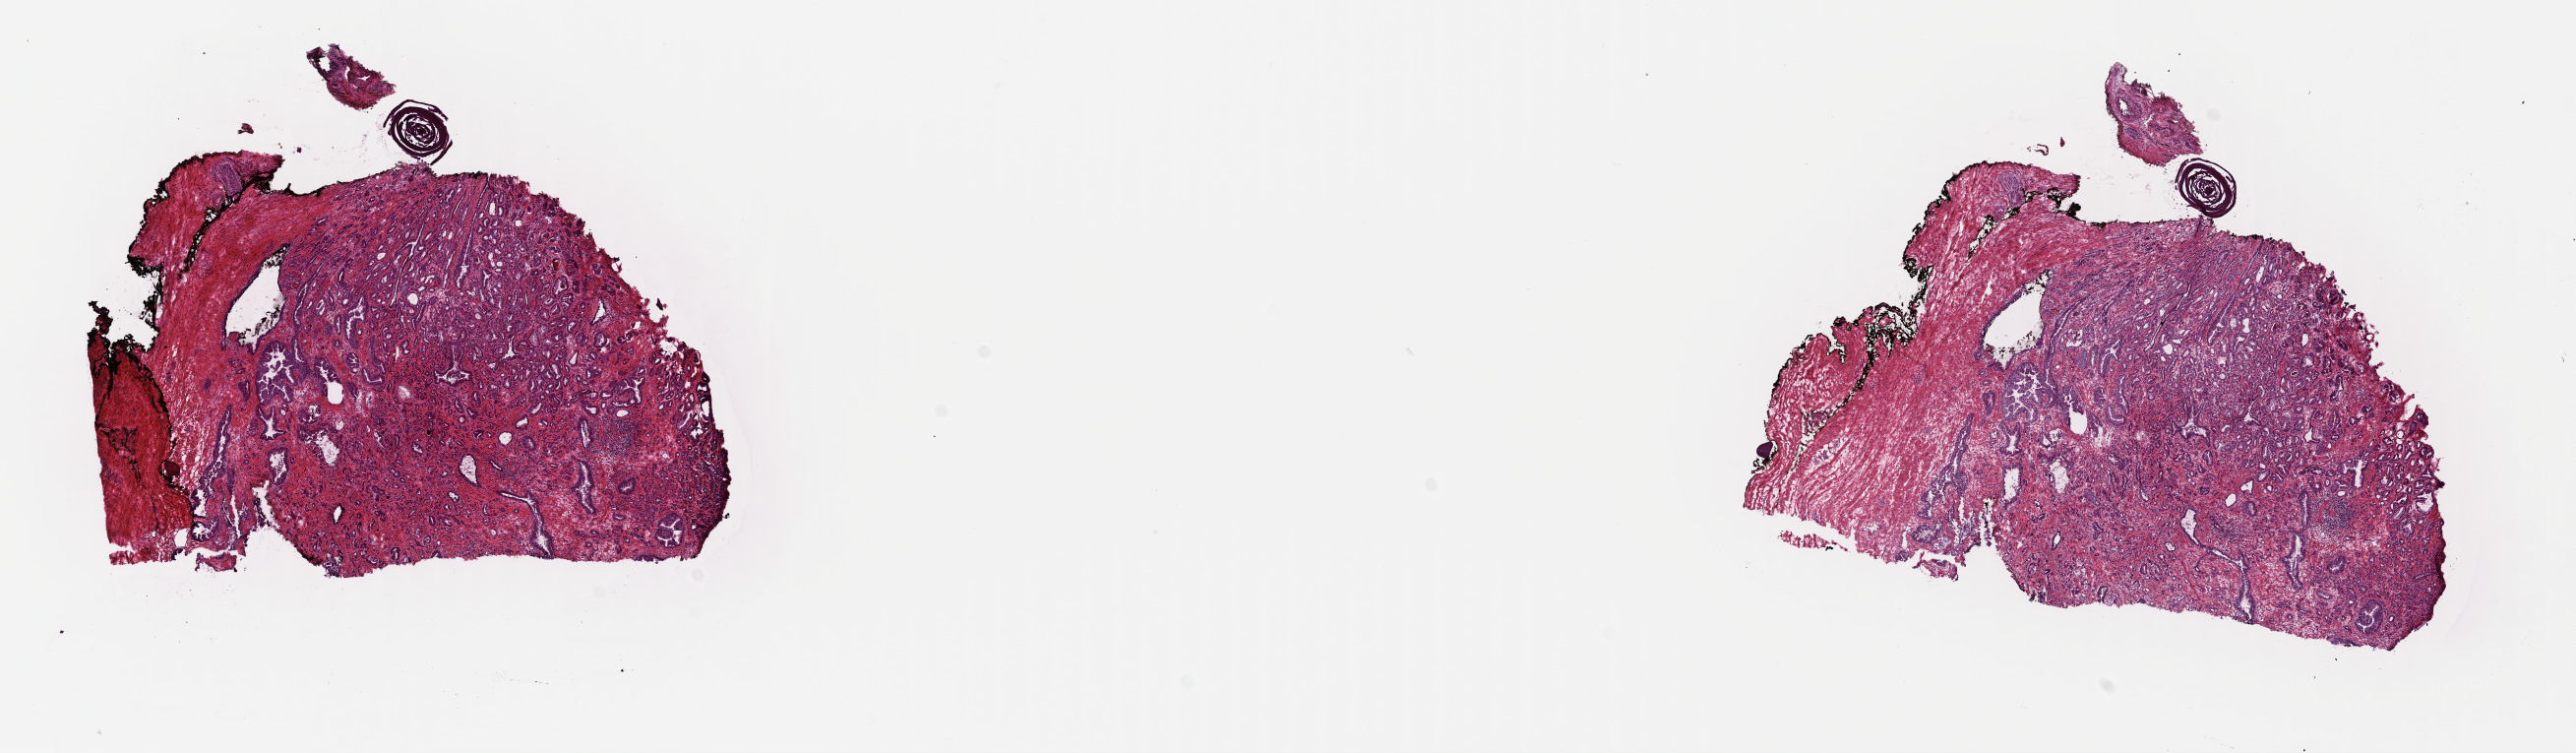
Whole-slide histology image, Hematoxylin and eosin (H&E) stained — shown as a low-resolution overview of the whole scanned area (about 20.6 x 6.0 mm, slide scanned at 40x), frozen section, sample: primary tumour, prostate. Male, age 70 years at initial diagnosis. Gleason score: 7 (3+4). Pathologist review of this section (percent, as recorded): tumour cells 70%, tumour nuclei 70%, normal cells 5%, stromal cells 25%, necrosis 0%. Inflammatory infiltration, as recorded: lymphocyte infiltration 40%, monocyte infiltration 20%, neutrophil infiltration 20%.
* pathologic diagnosis: Adenocarcinoma, NOS (prostate gland)